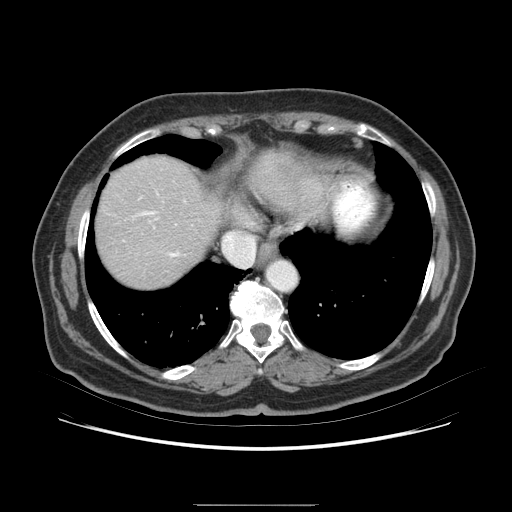
Contrast-enhanced abdominal CT (liver protocol), one axial slice; position 70 of 79 along the scan axis; soft-tissue window (W 400 / L 40 HU); 512 × 512 image matrix, field of view 380 × 380 mm. From the clinical record (not read from this slice): diagnosis: hepatocellular carcinoma (patient treated with transarterial chemoembolisation; whether this scan precedes or follows treatment is not stated here); TNM stage (as recorded): Stage-I; Child-Pugh class: A.
Outlined on this slice (semi-automatically segmented with operator editing):
- liver parenchyma outside the tumour (the mass and vessels are separate outlines, so this box may not span the whole liver): box from (x=106, y=164) to (x=198, y=266) px